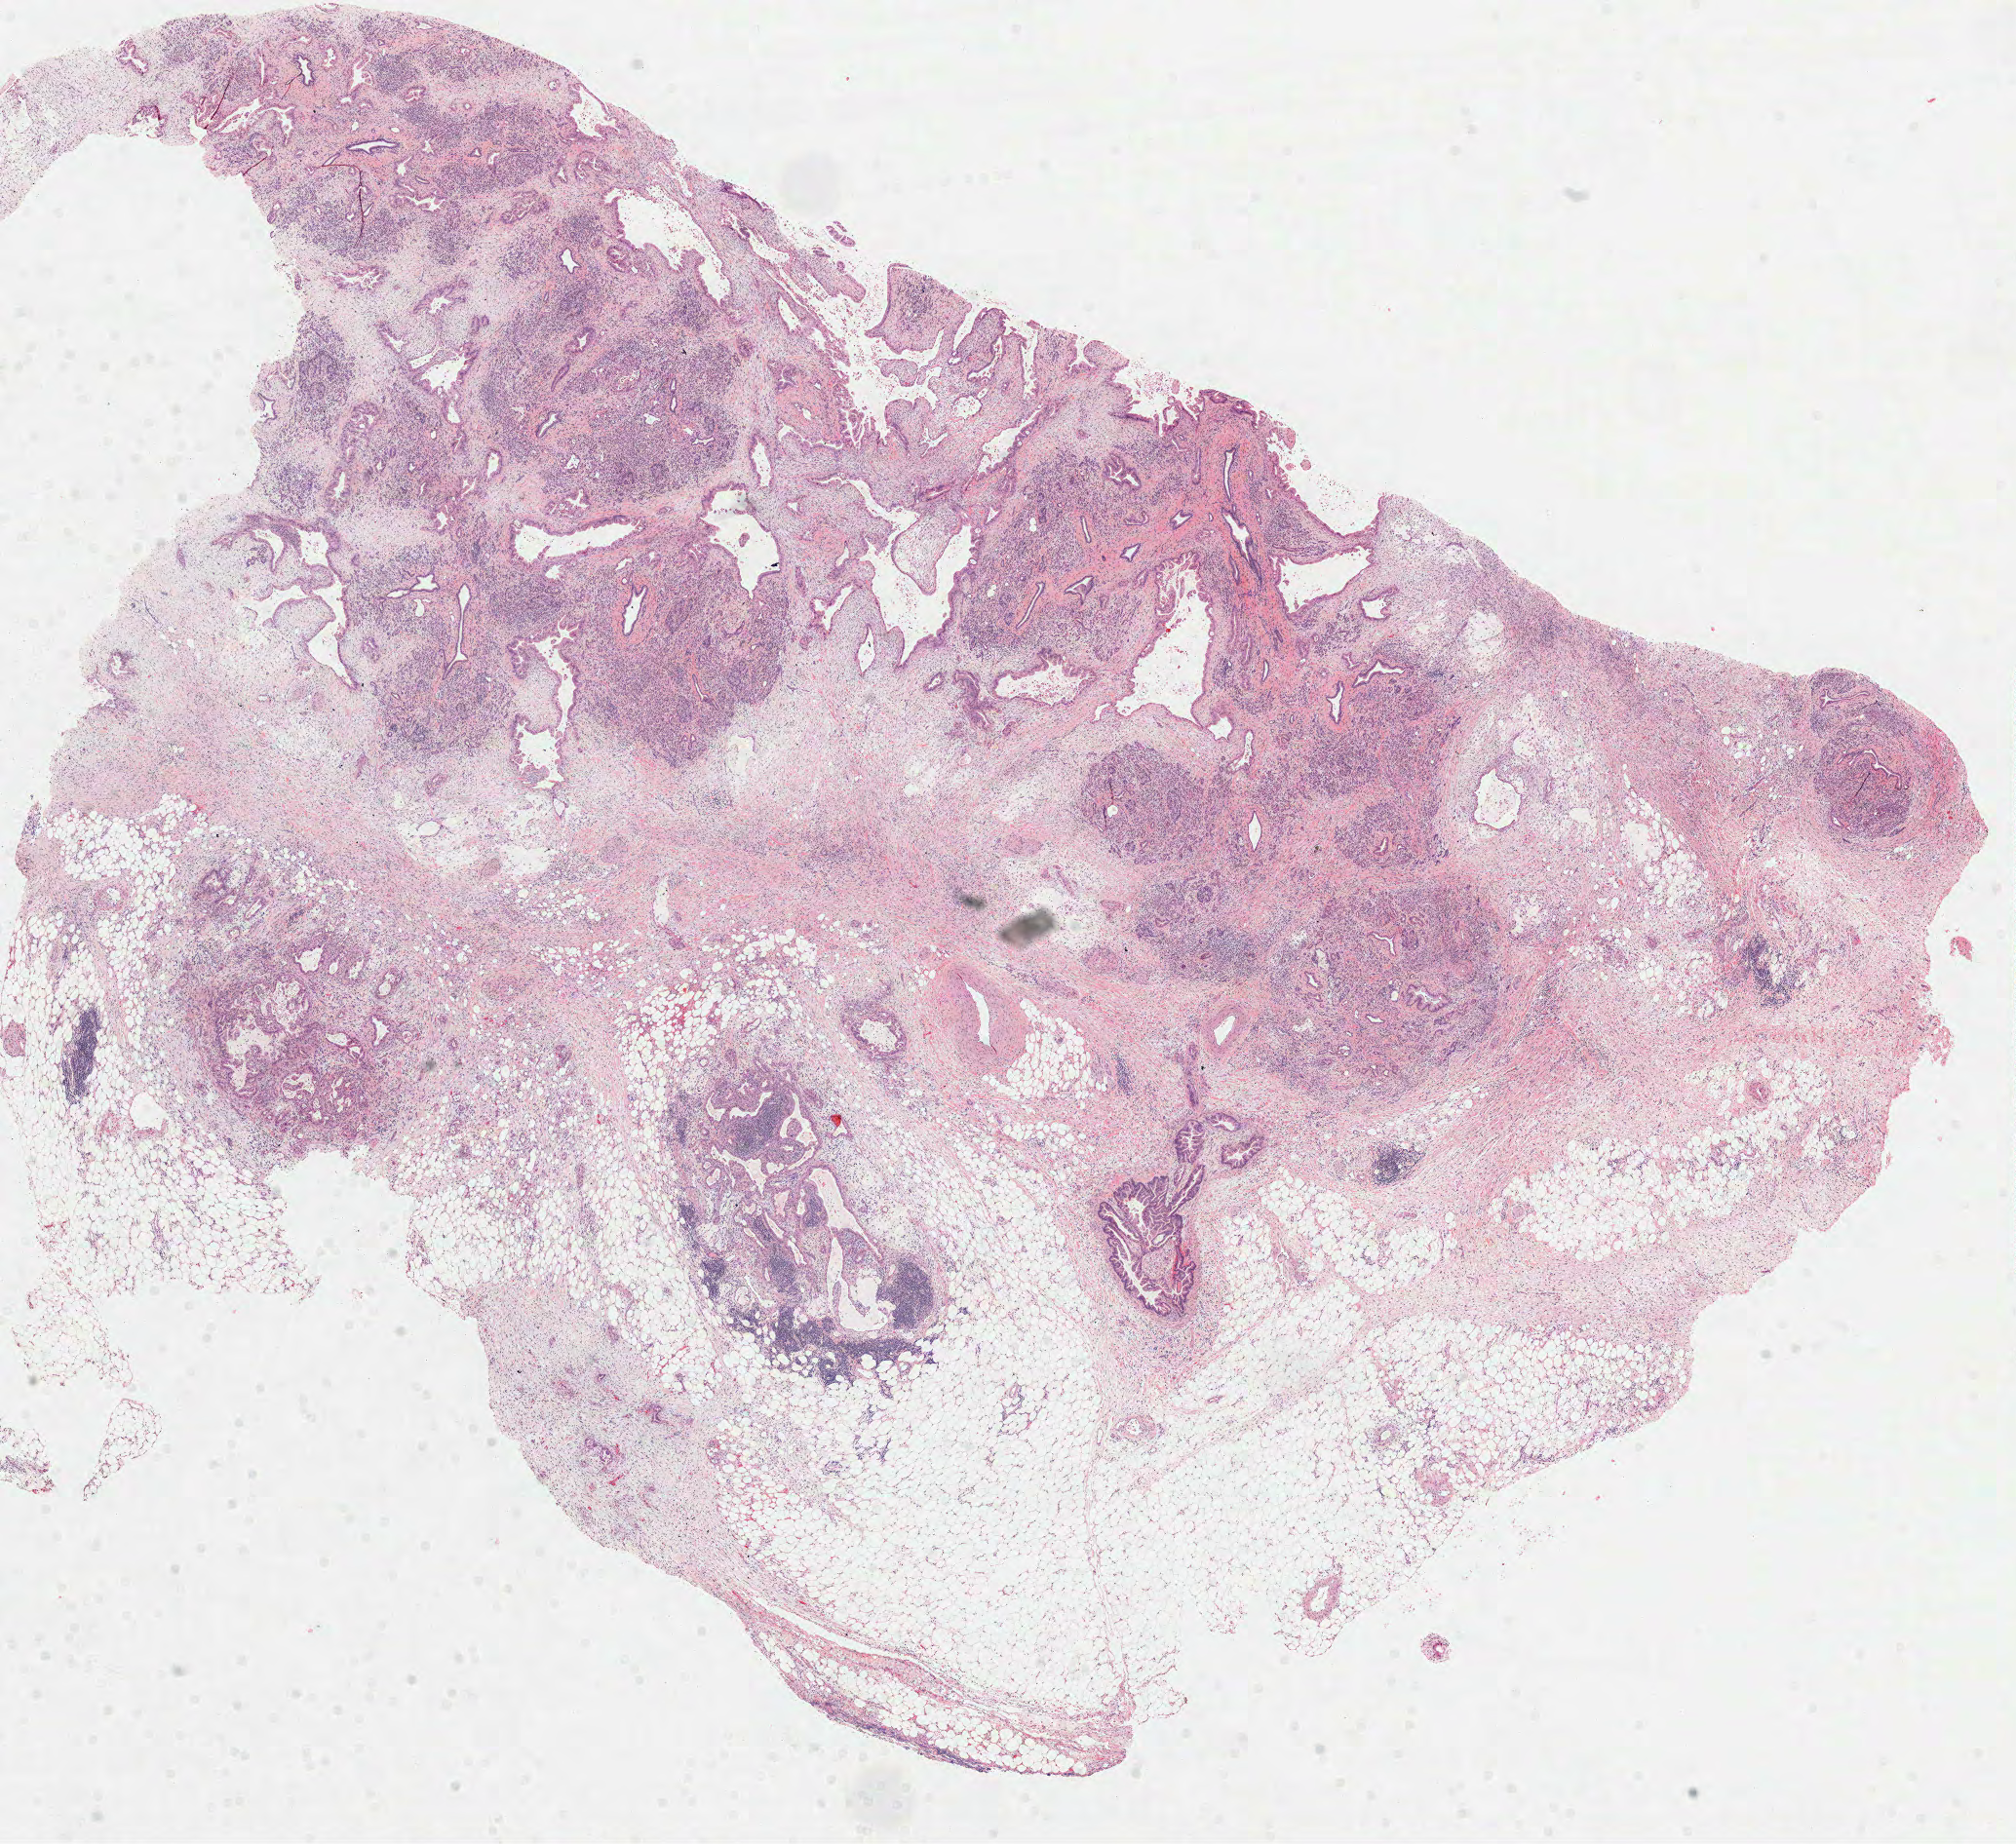
Digitized Hematoxylin and eosin (H&E) stained tissue section (whole slide), a low-resolution overview of the entire scanned area, about 16.7 x 15.3 mm; formalin-fixed paraffin-embedded (FFPE) diagnostic section; primary tumour sample from the pancreas. Male, age 64 years at initial diagnosis. Histologic grade: G1 (well differentiated).
AJCC pathologic stage: IIB. Diagnosis: Adenocarcinoma, NOS. Lymph nodes positive (case pathology): 9 of 17 examined.